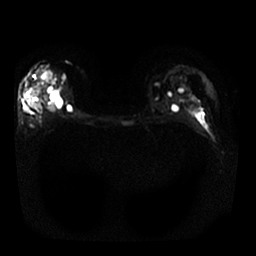
Breast MRI, one axial slice. Position 17 of 30 along the scan axis. Diffusion-weighted series; image 2 of 4 stored at this slice position (different b-values; order by instance number). 1.5 T. 4 mm slice thickness. 256 × 256 image matrix, field of view 340 × 340 mm. Female patient.
Outlined on this slice (manually delineated by an expert):
- tumour on diffusion-weighted imaging: bounding box <41,65,55,85> (left, top, right, bottom; pixels)